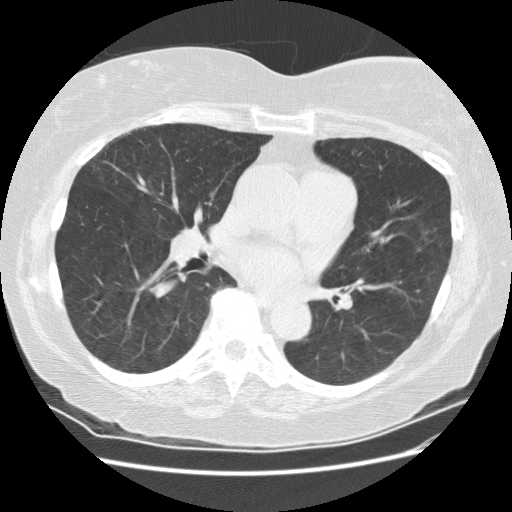
Low-dose screening chest CT, one axial slice. Position 93 of 180 along the scan axis. Reconstruction kernel STANDARD. 120 kVp. Lung window (W 1500 / L -600 HU). 512 × 512 image matrix, field of view 360 × 360 mm.
Annotated regions visible in this slice (expert manual segmentation):
- lesion 1 (tumor, upper lobe of left lung): bounding box <417,247,421,252> (left, top, right, bottom; pixels)